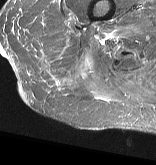
MRI of an extremity soft-tissue mass, one axial slice. Position 12 of 57 along the scan axis. STIR. MR volume resampled by the dataset authors to the PET/CT grid (not the native acquisition matrix). 3.27 mm slice thickness. 156 × 165 image matrix, field of view 152 × 161 mm. Female patient. From the clinical record (not read from this slice): histological type: epithelioid sarcoma with vascular differentiation; site of the primary tumour: right buttock.
Annotated regions visible in this slice (expert contour drawn on MRI and transferred to this co-registered scan by the dataset authors):
- gross tumour volume (mass): bounding box [x1, y1, x2, y2] px = [49, 35, 77, 93]